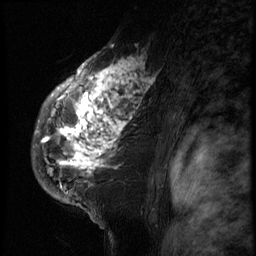
Breast MRI (dynamic contrast-enhanced), one sagittal slice. Position 49 of 66 along the scan axis. 3 images stored at this slice position (order not interpretable as contrast timing). 1.5 T. TE 4.2 ms, TR 8.9 ms. 2.5 mm slice thickness. 256 × 256 image matrix. Patient: female, 39 years. From the clinical record (not read from this slice): setting: breast cancer imaged before/during neoadjuvant chemotherapy; receptor status: HER2-positive.
Structures marked on this image (semi-automatically segmented with operator editing):
- analysis volume of interest (the breast-tissue region the enhancement analysis was run in; not a lesion): box from (x=31, y=44) to (x=166, y=196) px
- tumour enhancement mask (voxels above the 140 % enhancement threshold inside the analysis volume of interest): (x=41, y=45)–(x=154, y=171)